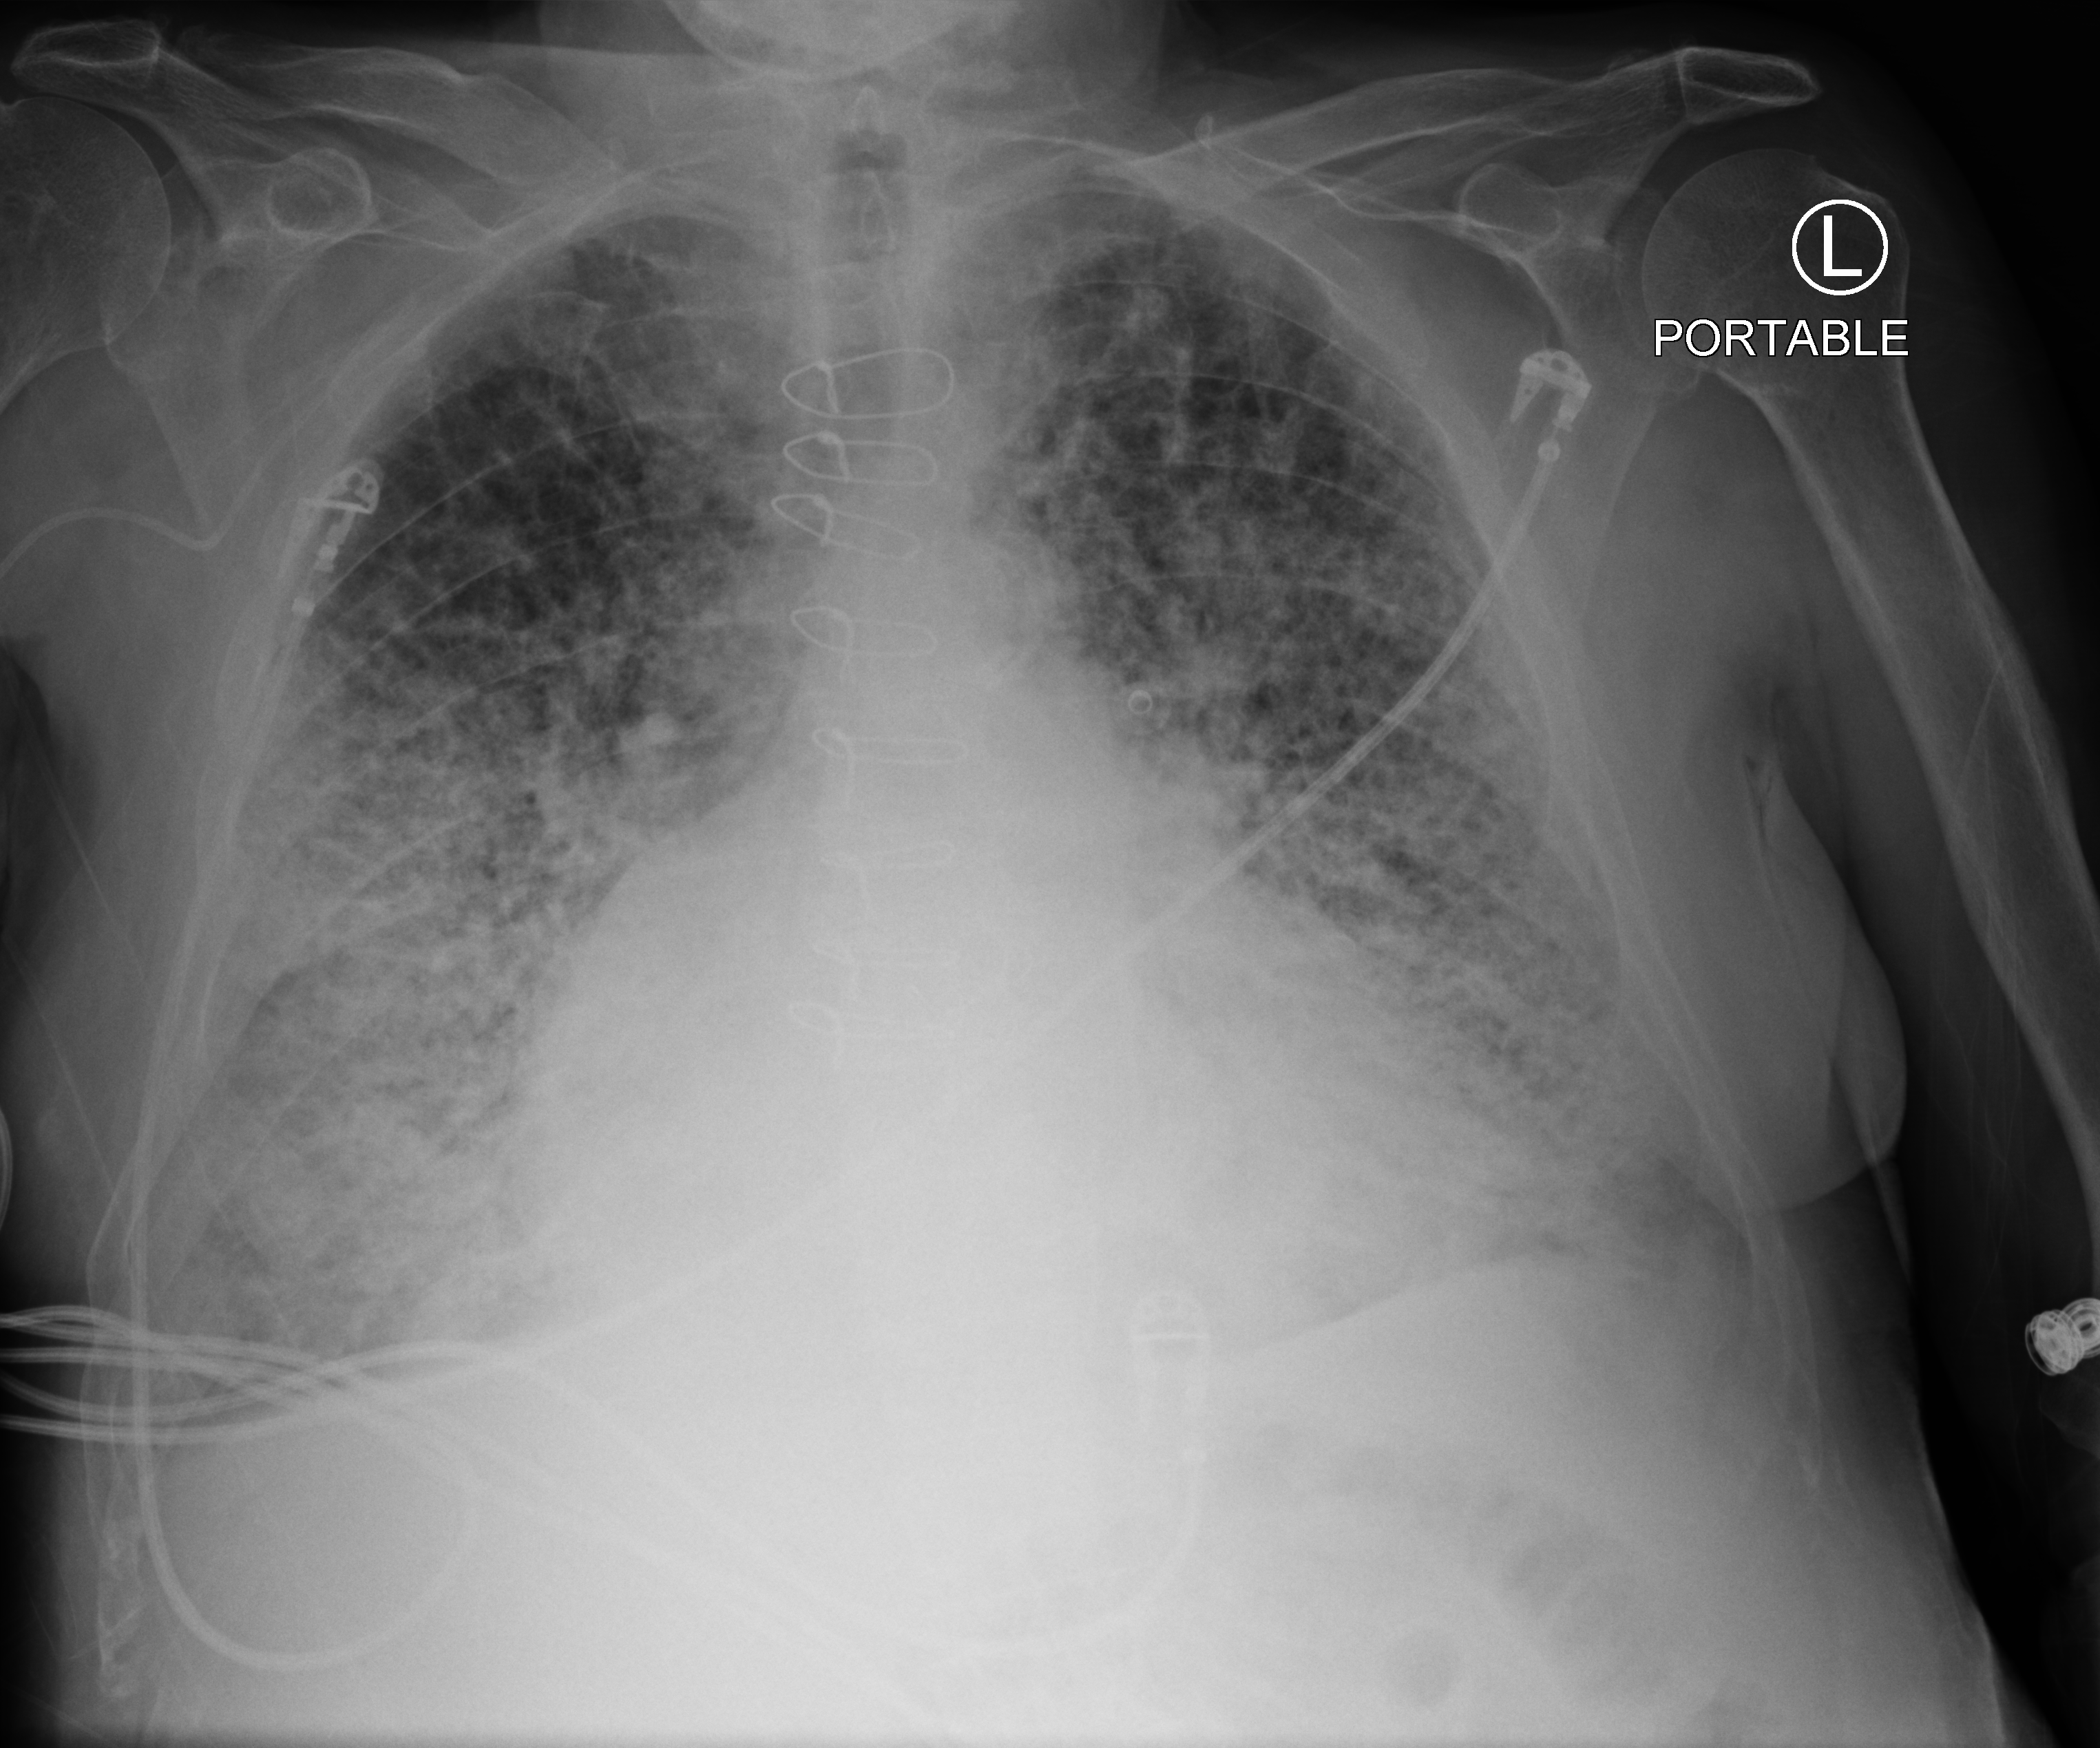
Chest X-ray (portable), anteroposterior (AP) projection. Male patient hospitalised with COVID-19, age 75–90 years.
Admission-level facts for this patient (not findings on this image; timing relative to this image not recorded):
- mechanically ventilated during this hospital stay: yes